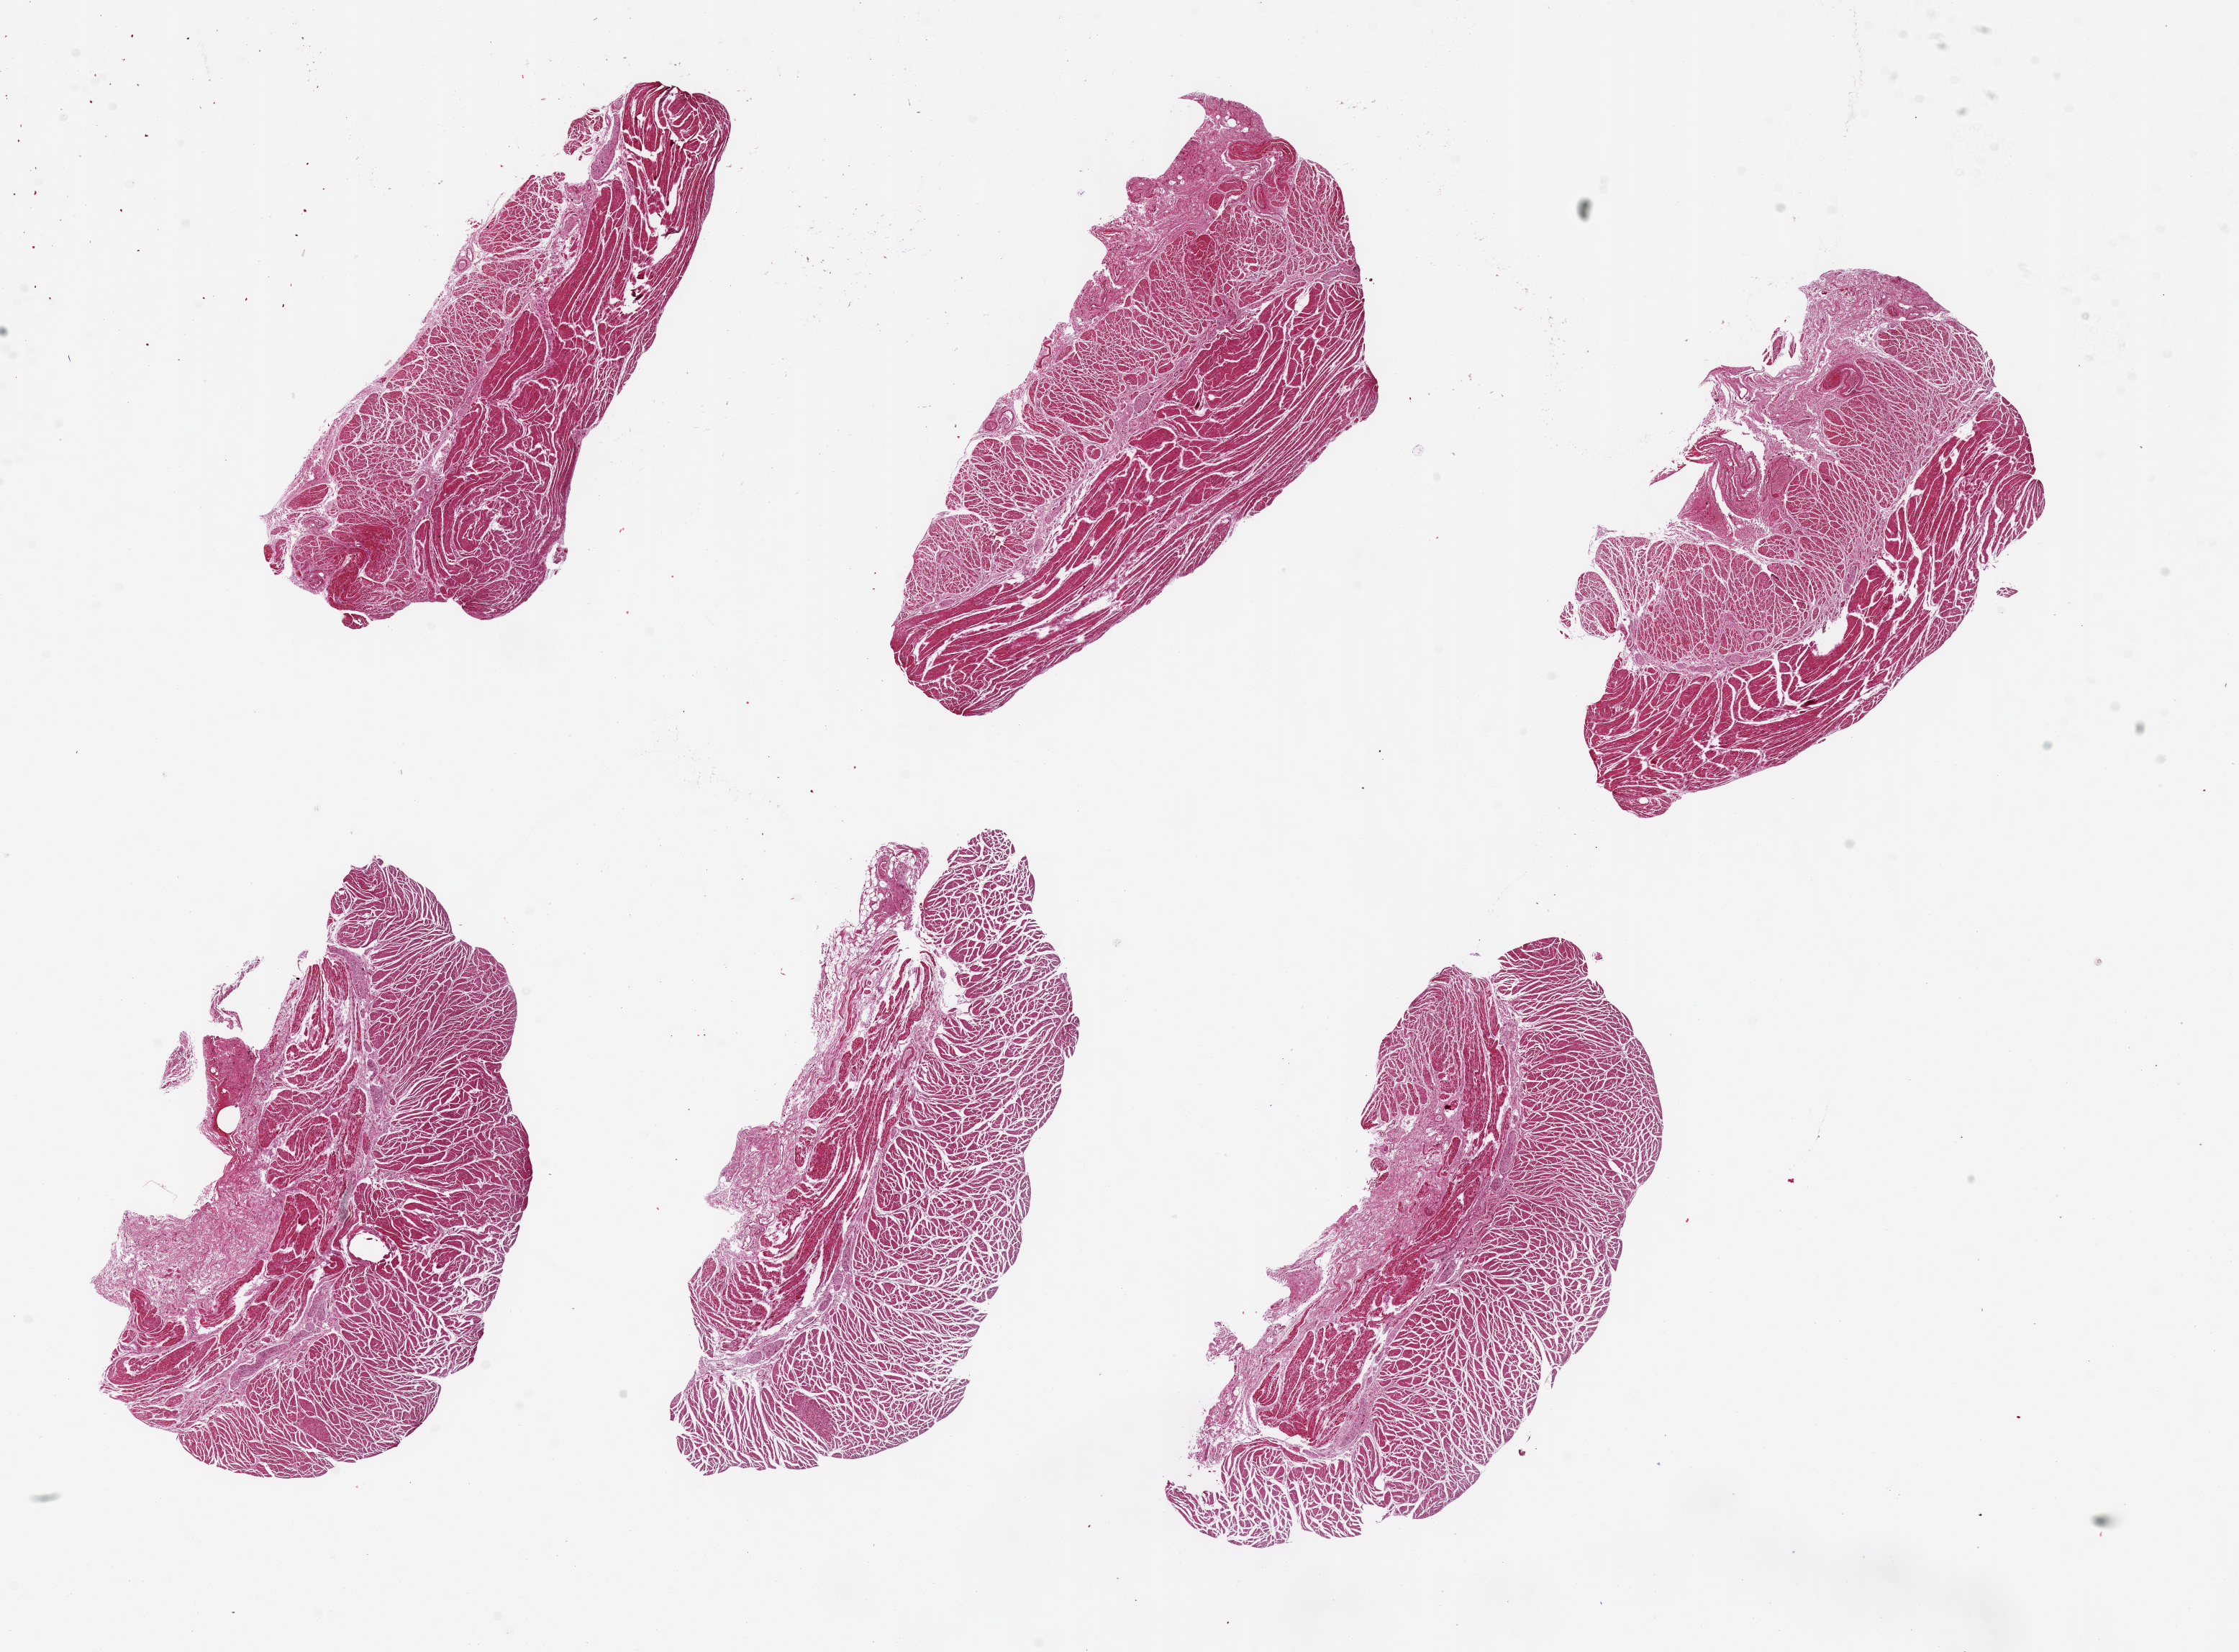
H&E whole-slide image — whole scanned area (about 24.6 x 18.2 mm) shown as a low-resolution overview; PAXgene-fixed paraffin-embedded (PFPE) section; sampled site (target tissue): gastroesophageal junction; tissue donor sample. Donor sex: female.
Pathologist's review note for this sample: 6 pieces, up to 8x3mm; good specimens, all muscularis, just autolyzed.